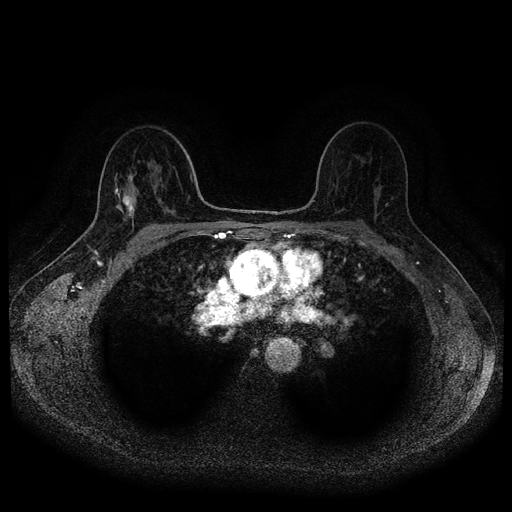
Breast MRI (dynamic contrast-enhanced, multi-phase), one axial slice. Slice 65 of 116 in the series (ordered by position). Dynamic contrast-enhanced series, time point 2 of 5 at this slice position (early post-contrast). 1.5 T. TE 2.6 ms, TR 5.4 ms. 2 mm slice thickness. 512 × 512 image matrix, field of view 340 × 340 mm. Female patient, age 49 years.
Outlined on this slice (semi-automatically segmented with operator editing):
- breast lesion (labelled 'tumour' in the annotation; benign lesions carry a separate 'benign' label): bounding box <118,188,137,216> (left, top, right, bottom; pixels)